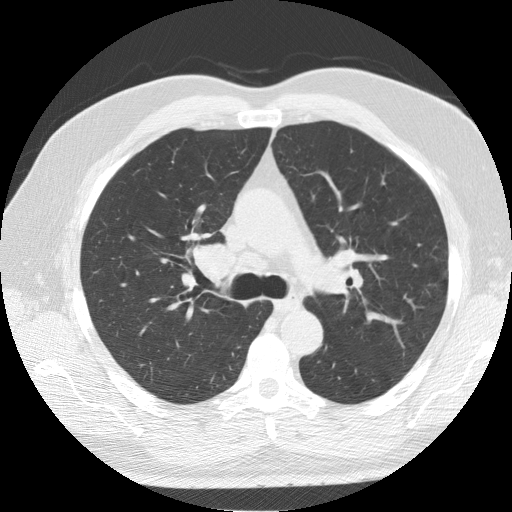
Axial slice from a low-dose chest CT screening exam, second screening round (one year after baseline), lung window (W 1500 / L -600 HU), standard (soft-tissue) reconstruction kernel (STANDARD), 512 × 512 image matrix. Male, age 64 years at enrolment. Former smoker at enrolment.
• Expert reader's lesion annotation, bounding box <172,226,253,303> (left, top, right, bottom; pixels).
• Reader record for this screening exam (exam-level; its link to the box is not recorded): non-calcified nodule or mass ≥4 mm, right lower lobe, 7 × 5 mm, smooth margins, soft tissue attenuation, pre-existing on the prior screen: yes; interval growth: no.
• Participant outcome: lung cancer diagnosed 63 days after this screen — adenocarcinoma, NOS, right upper lobe, poorly differentiated (G3), stage IB (AJCC 6th edition), 37 mm at pathology.